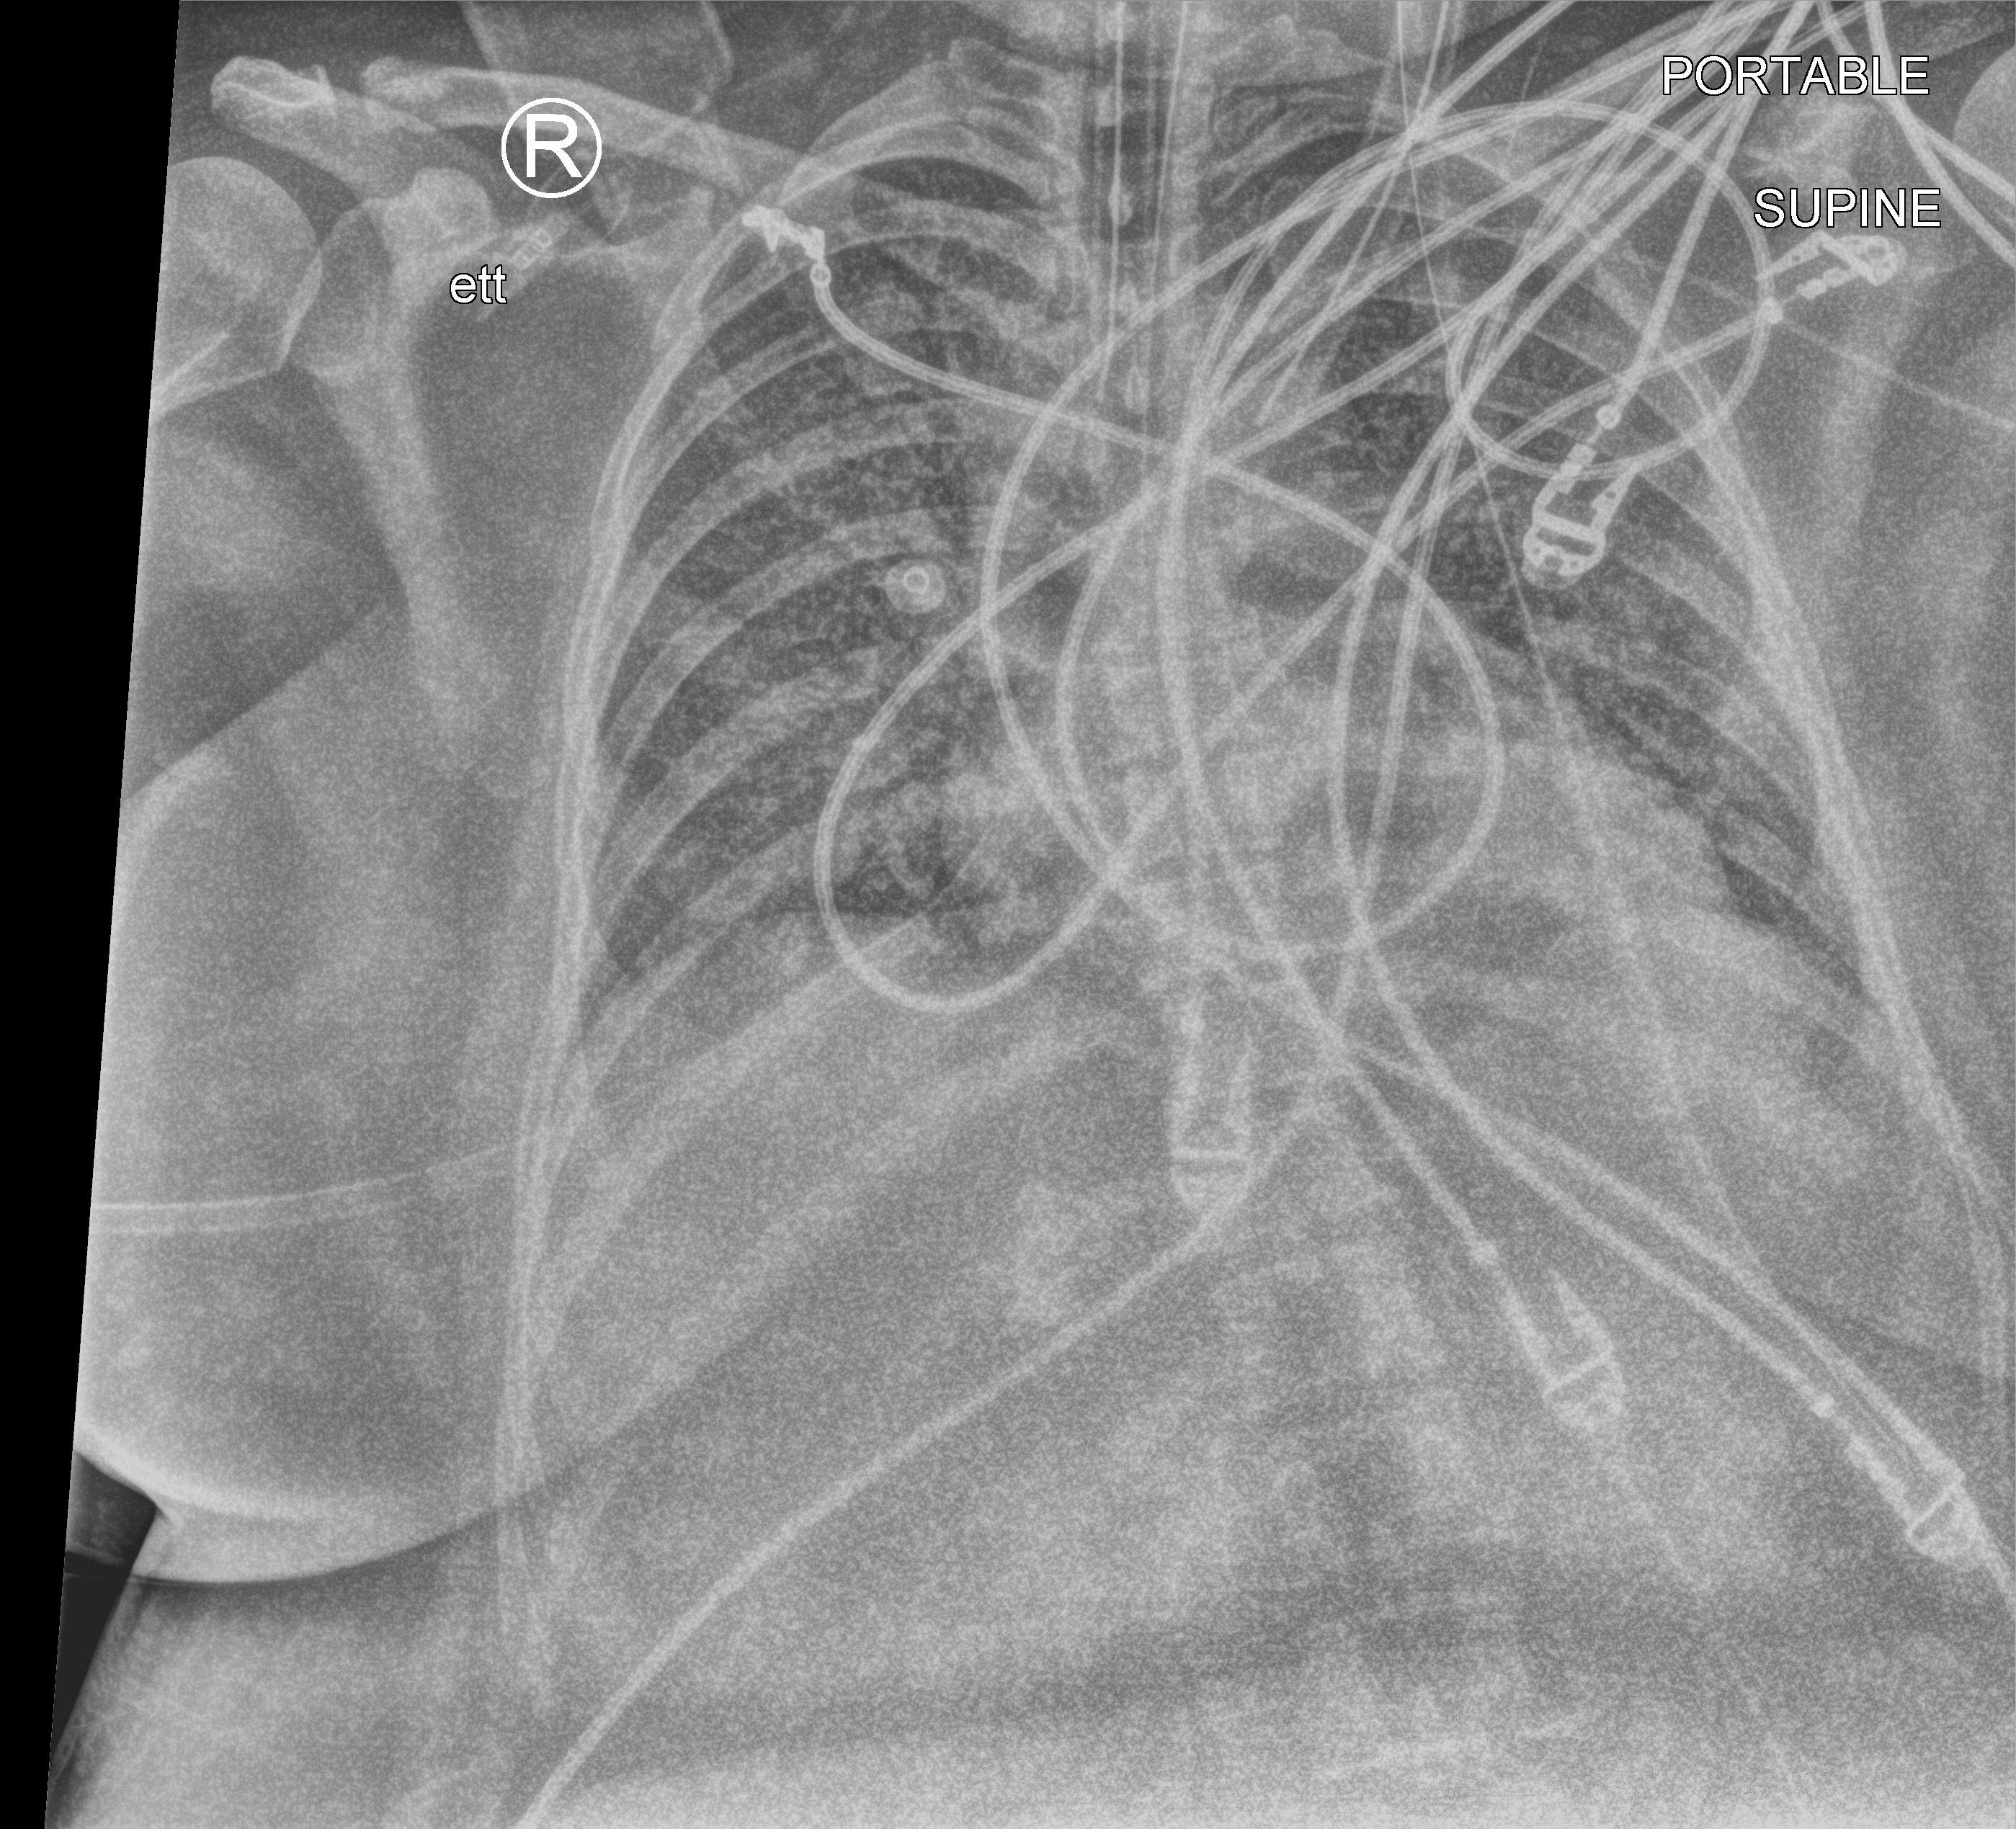
Chest X-ray (portable), anteroposterior (AP) projection. Patient hospitalised with COVID-19; female, aged 18–59 years.
Admission-level facts for this patient (not findings on this image; timing relative to this image not recorded): other chronic lung disease (admission record): no; diabetes (admission record): no; mechanically ventilated during this hospital stay: yes.